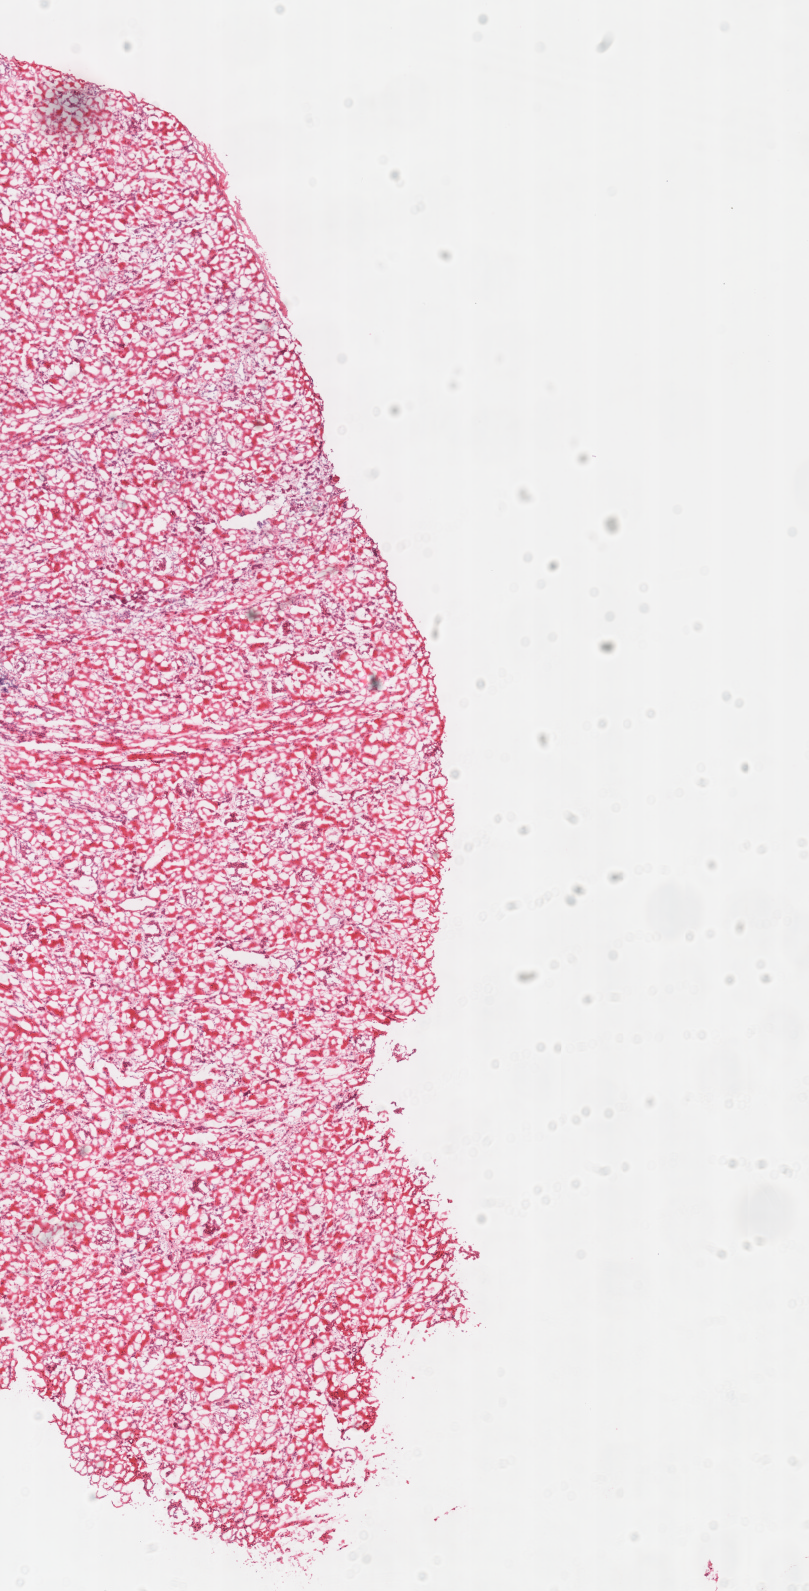
H&E-stained whole-slide image, a low-resolution overview of the entire scanned area, about 6.4 x 12.5 mm. Frozen section. Sample: solid tissue normal (non-tumour tissue), kidney. Female, age 65 years at initial diagnosis. Infiltration values recorded for this section: lymphocyte infiltration 0%, monocyte infiltration 0%, neutrophil infiltration 0%.
• this section: solid tissue normal sample (biorepository sample class)
• patient diagnosis: Renal cell carcinoma, chromophobe type